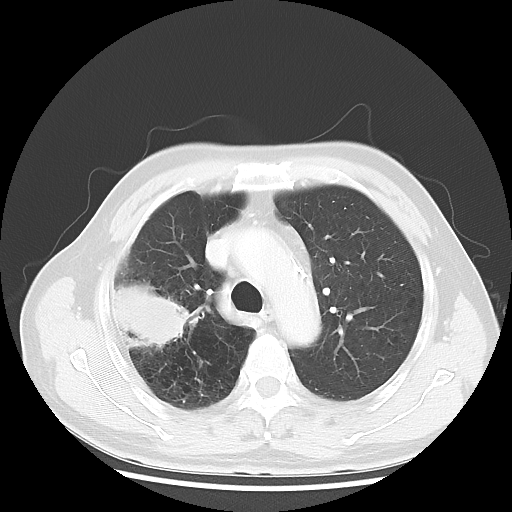
Chest CT, one axial slice. Slice 36 of 50 in the series (ordered by position). Reconstruction kernel LUNG. Lung window (W 1500 / L -600 HU). 512 × 512 image matrix. Patient: male, 69 years. From the clinical record (not read from this slice): clinical TNM (as recorded): T3 N0 M0; histopathological grade: G3.
Structures marked on this image (bounding box drawn by a radiologist):
- lung tumour (recorded histology: adenocarcinoma): box from (x=109, y=276) to (x=201, y=352) px